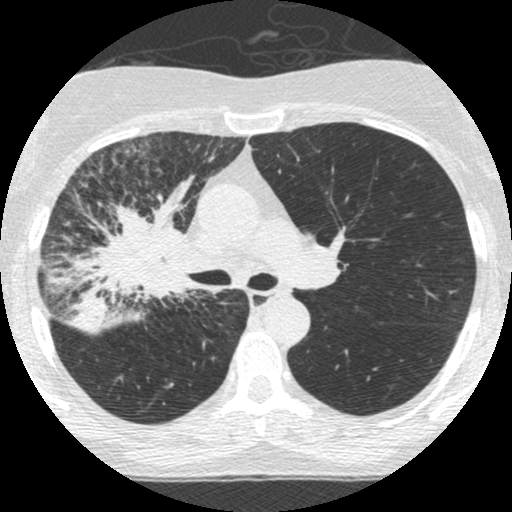
Low-dose screening chest CT, one axial slice; position 165 of 253 along the scan axis; 120 kVp; lung window (W 1500 / L -600 HU); 512 × 512 image matrix, field of view 294 × 294 mm.
Structures marked on this image (expert manual segmentation):
- lesion 2 (tumor, hilum of right lung): bounding box [x1, y1, x2, y2] px = [49, 173, 196, 328]